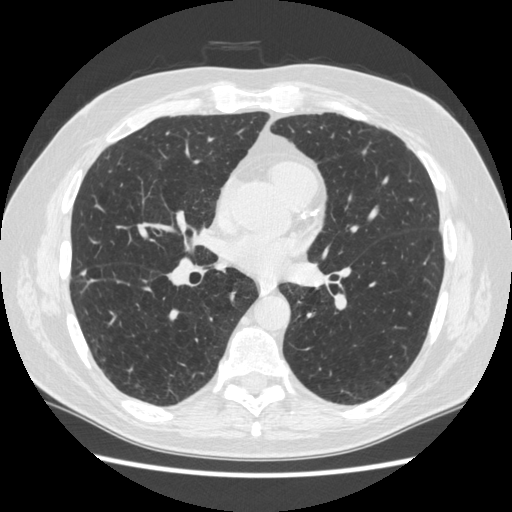
Low-dose screening chest CT, one axial slice. Slice 129 of 267 in the series (ordered by position). Reconstruction kernel STANDARD. Lung window (W 1500 / L -600 HU). 512 × 512 image matrix, field of view 360 × 360 mm.
Outlined on this slice (expert manual segmentation):
- lesion 2 (nodule, lower lobe of right lung): bounding box [x1, y1, x2, y2] px = [81, 271, 86, 275]